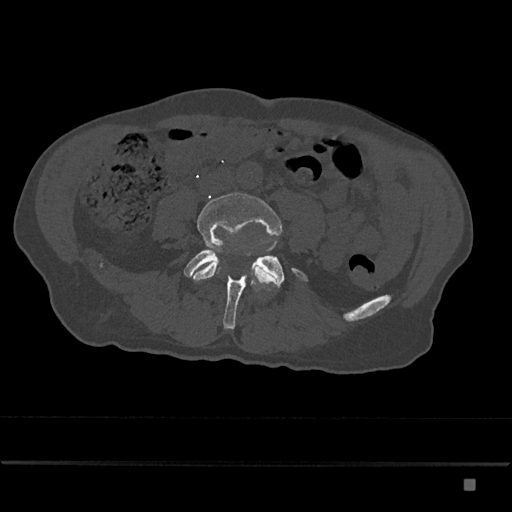
CT including the spine, one axial slice; slice 307 of 797 in the series (ordered by position); bone window (W 1800 / L 400 HU); 0.5 mm slice thickness; 512 × 512 image matrix, field of view 390 × 390 mm. Male patient, age 72 years. From the clinical record (not read from this slice): primary cancer: prostate.
Outlined on this slice (semi-automatically segmented with operator editing):
- L4 vertebra: bounding box (x1, y1, x2, y2) in pixels: (188, 192, 283, 285)
- L5 vertebra: (183, 245, 308, 330)